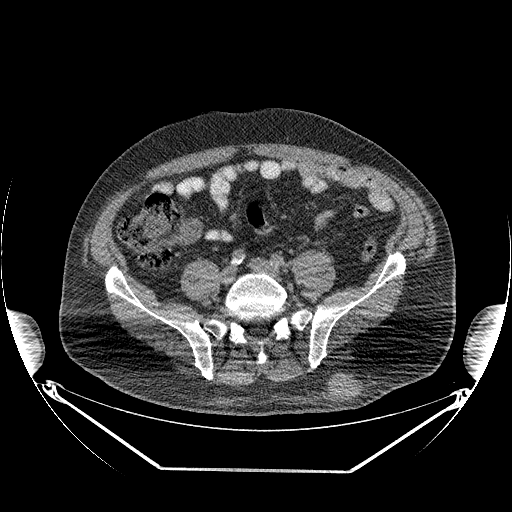
CT of an extremity soft-tissue mass (from a PET/CT study), one axial slice; 140 kVp; soft-tissue window (W 400 / L 40 HU); 3.75 mm slice thickness; 512 × 512 image matrix, field of view 500 × 500 mm. Male patient. From the clinical record (not read from this slice): histological type: pleiomorphic leiomyosarcoma; grade: high; site of the primary tumour: left buttock.
Outlined on this slice (expert contour drawn on MRI and transferred to this co-registered scan by the dataset authors):
- gross tumour volume including surrounding oedema: bounding box [x1, y1, x2, y2] px = [327, 375, 359, 405]
- gross tumour volume (mass): [327, 379, 355, 403]